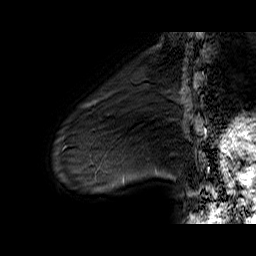
Breast MRI (dynamic contrast-enhanced), one sagittal slice; slice 11 of 60 in the series (ordered by position); dynamic contrast-enhanced series, time point 2 of 6 at this slice position (early post-contrast); 1.5 T; TE 6.5 ms, TR 32.9 ms; 256 × 256 image matrix, field of view 200 × 200 mm. Female patient. From the clinical record (not read from this slice): setting: breast cancer imaged before/during neoadjuvant chemotherapy; receptor status: HER2-positive.
Outlined on this slice (semi-automatic segmentation, software-assisted and operator-edited):
- analysis volume of interest (the breast-tissue region the enhancement analysis was run in; not a lesion): bounding box <72,88,133,137> (left, top, right, bottom; pixels)
- tumour enhancement mask (voxels above the 100 % enhancement threshold inside the analysis volume of interest): <82,92,112,108>